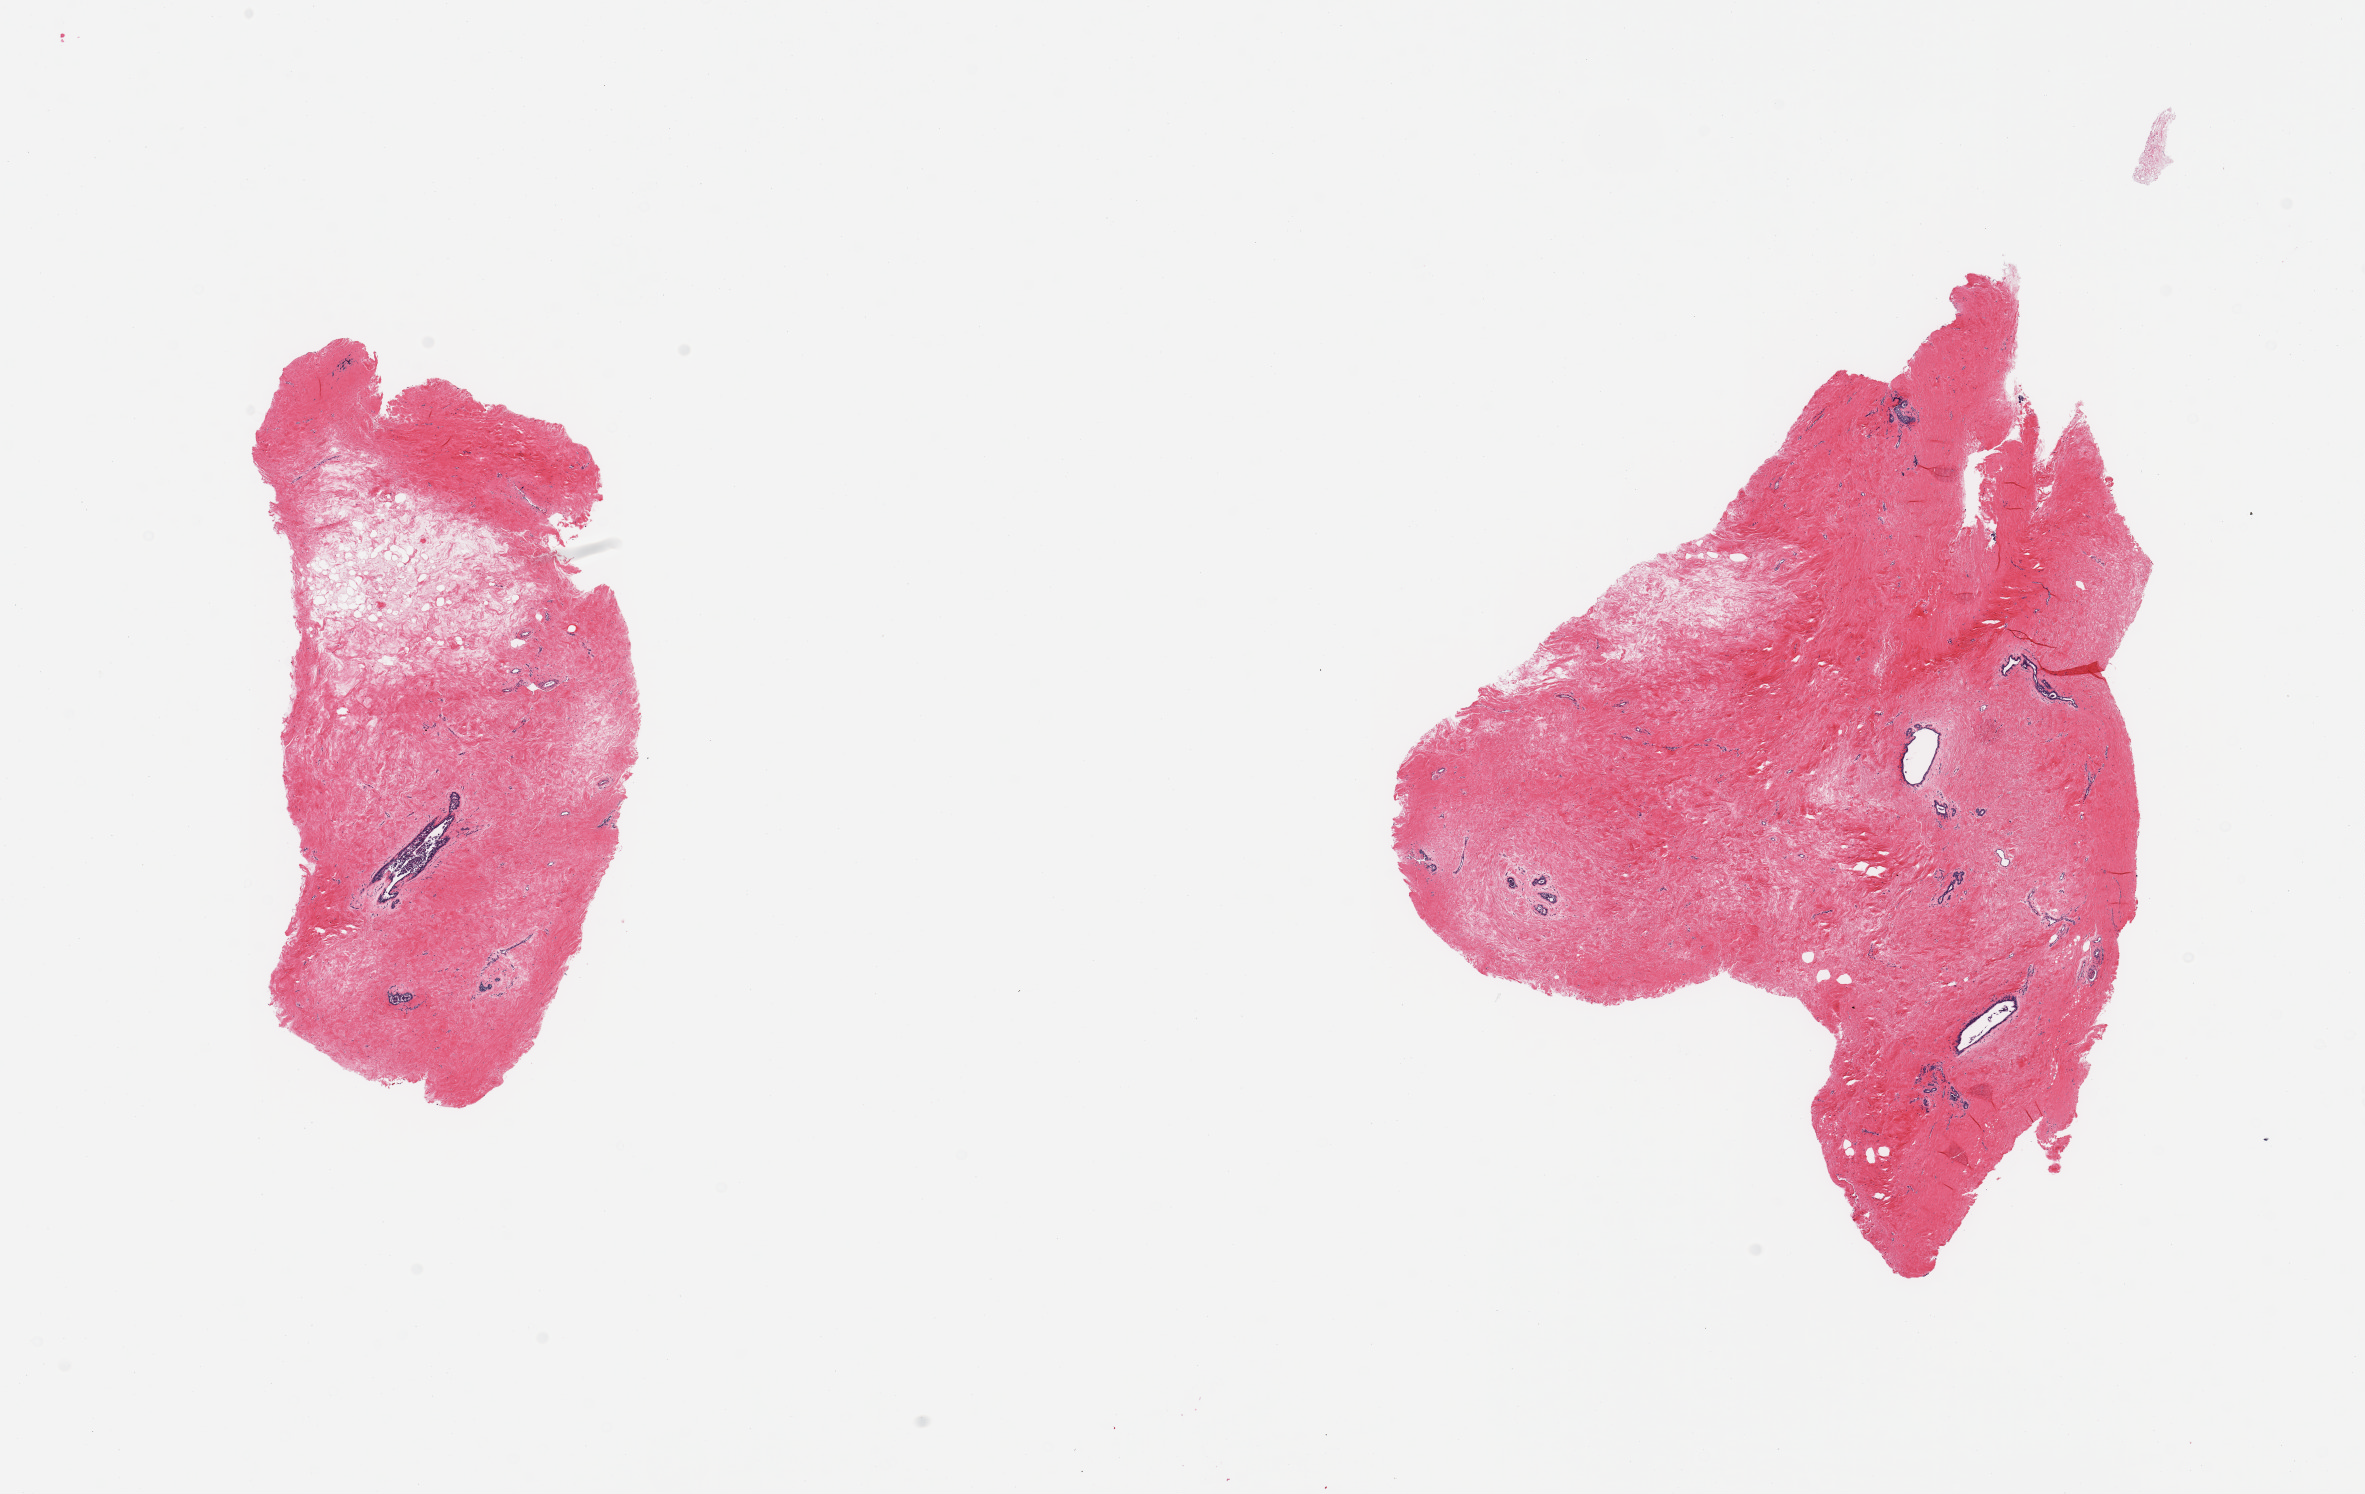
H&E whole-slide image, shown as a low-resolution overview of the whole scanned area (about 18.7 x 11.8 mm), PAXgene-fixed paraffin-embedded (PFPE) section, sampled site (target tissue): breast, tissue donor sample. Donor sex: male.
Review note (as recorded): 2 pieces; dense fibrocollagenous tissue with embedded ducts with gynecomastoid change.